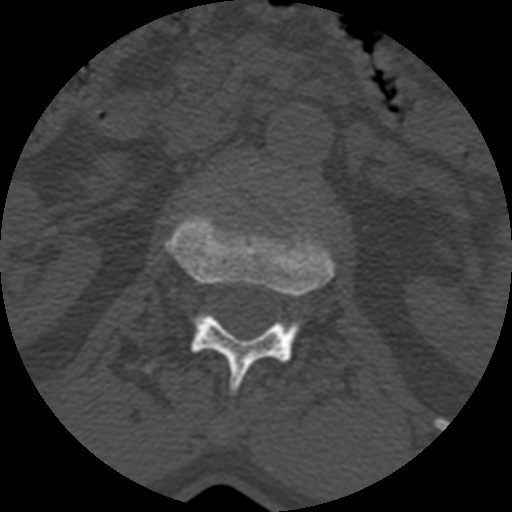
CT including the spine, one axial slice; slice 356 of 399 in the series (ordered by position); bone window (W 1800 / L 400 HU); 1.25 mm slice thickness; 512 × 512 image matrix, field of view 160 × 160 mm. Patient age 71 years. From the clinical record (not read from this slice): primary cancer: prostate.
Outlined on this slice (semi-automatic segmentation, software-assisted and operator-edited):
- L1 vertebra: box from (x=168, y=212) to (x=333, y=393) px